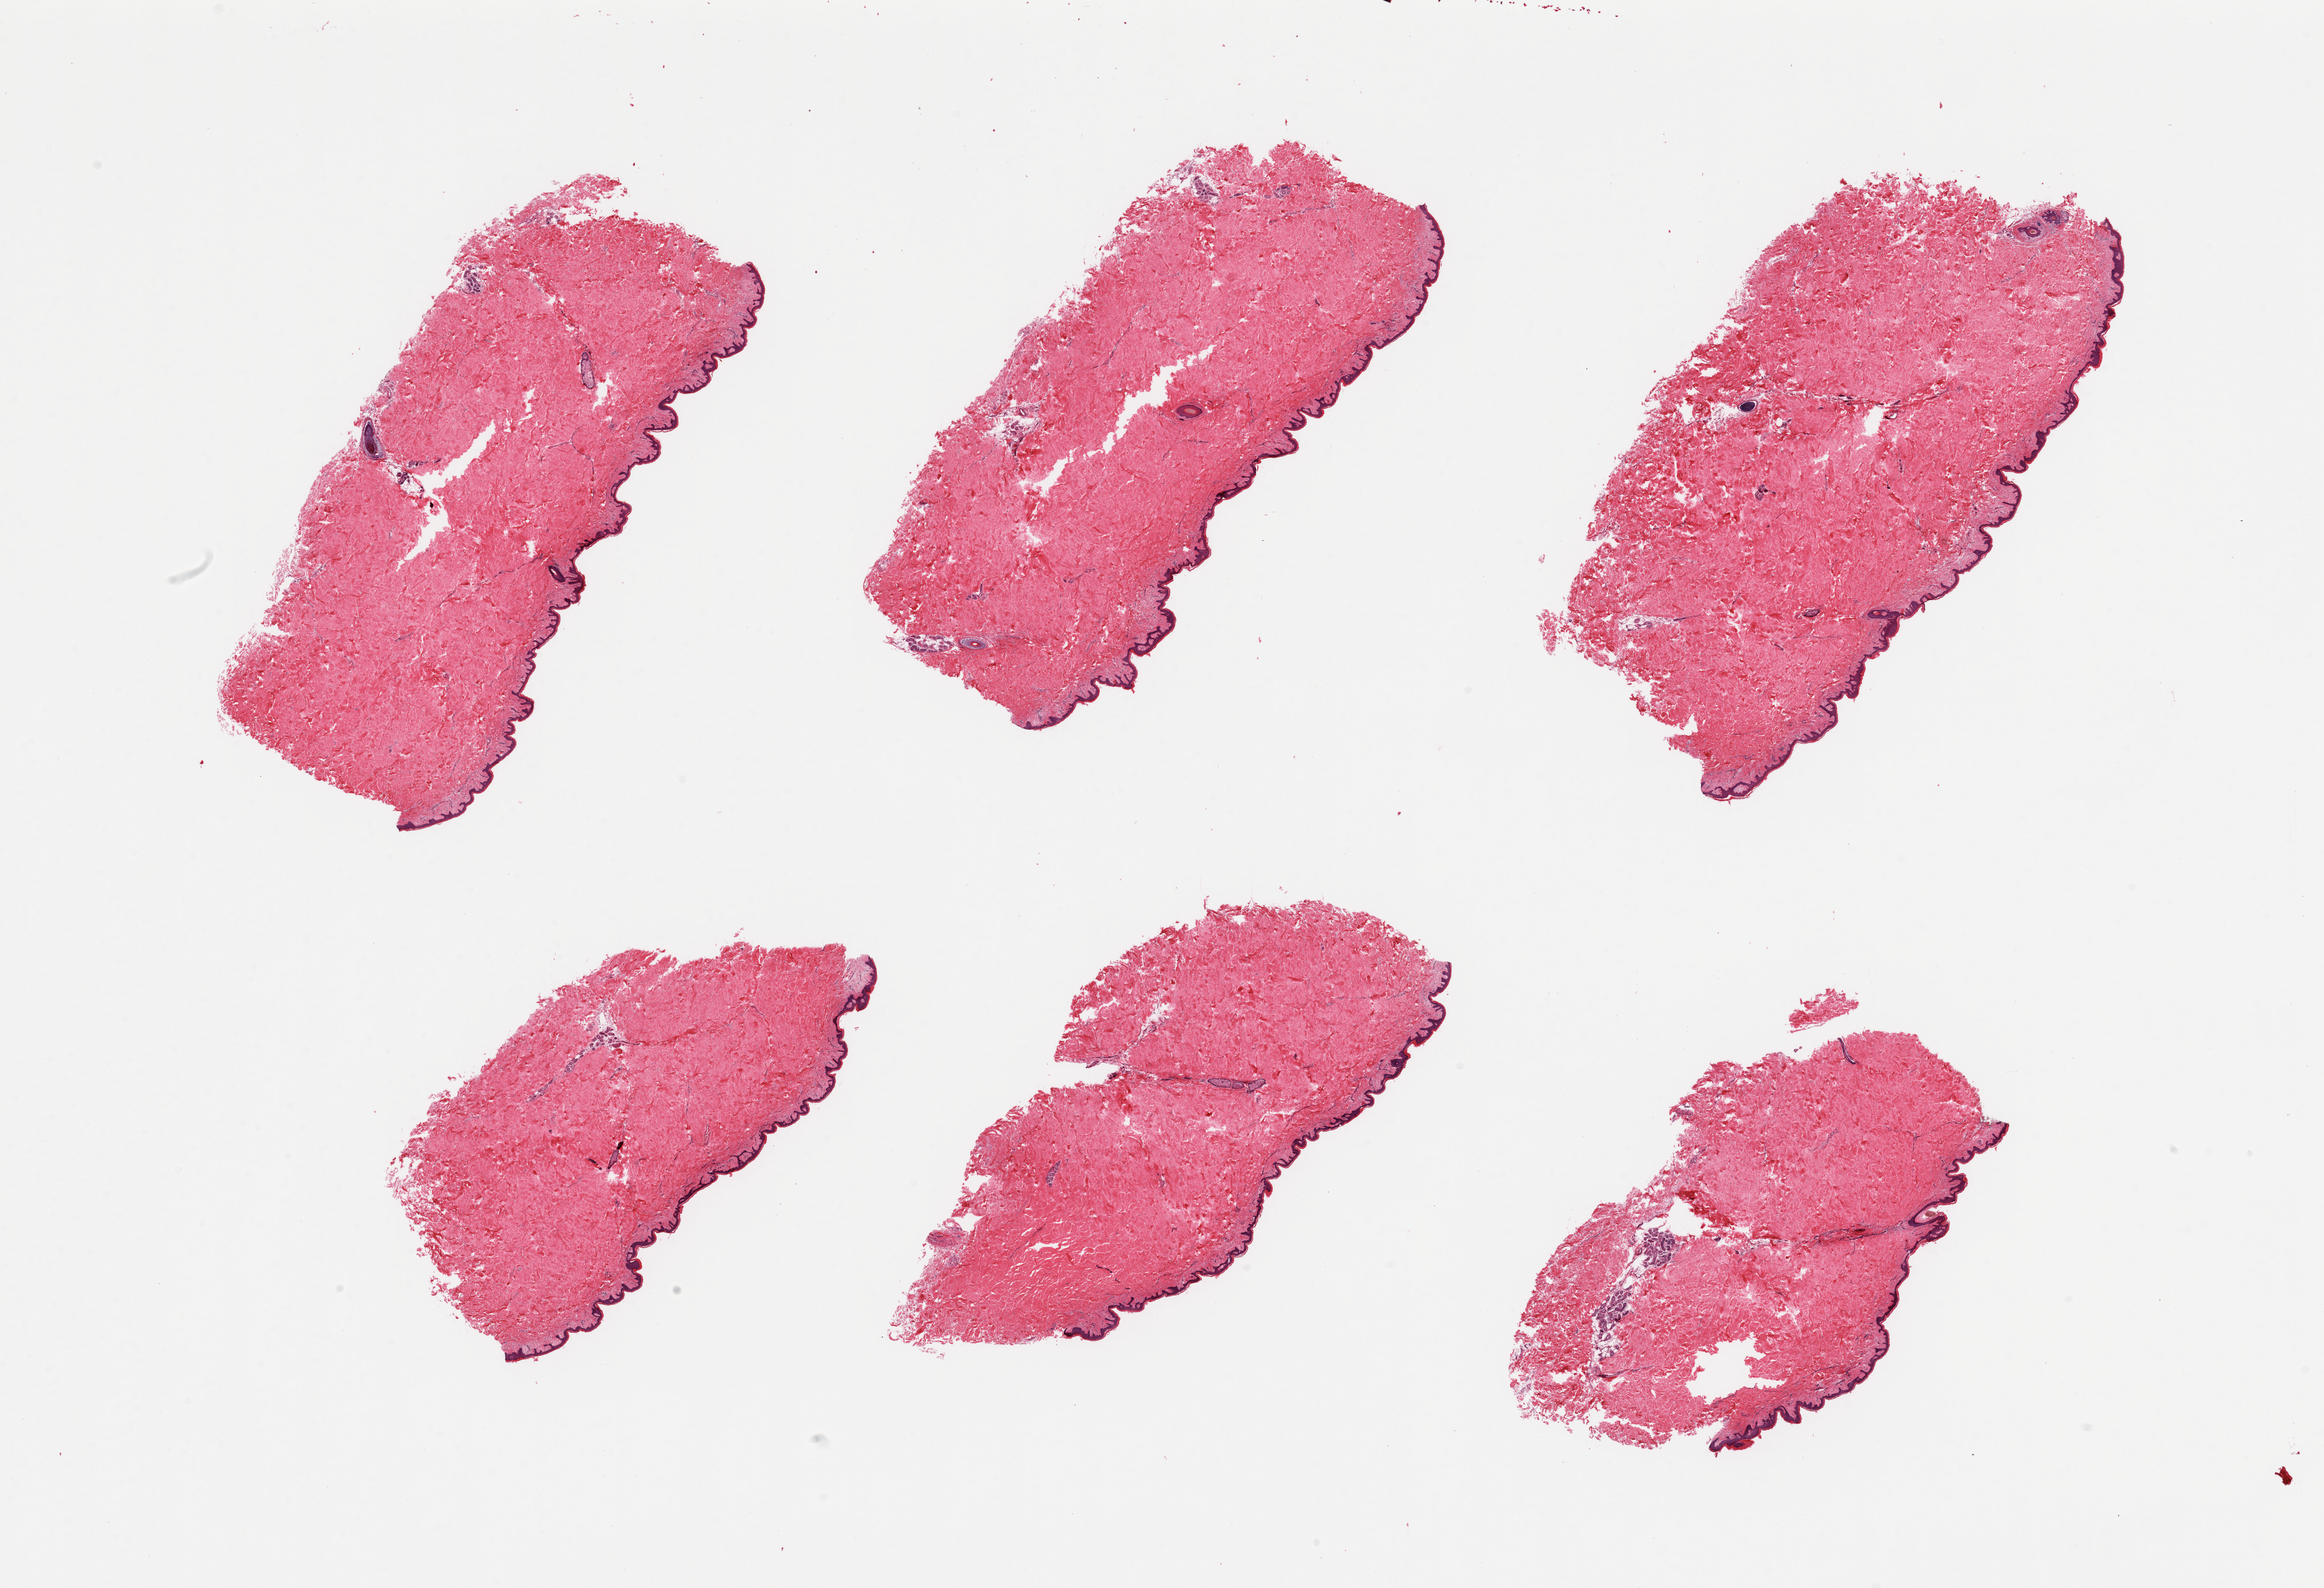
Digitized H&E-stained section, brightfield, low-resolution overview of the scanned area, about 29.5 x 20.2 mm, PAXgene-fixed paraffin-embedded (PFPE) section, section of skin of suprapubic region (target tissue), tissue donor sample. Donor: male.
• reviewer comment on this tissue sample: 6 pieces; well trimmed; no internal fat